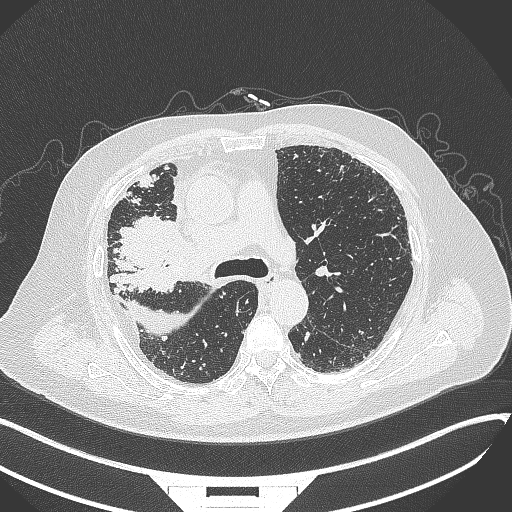
Chest CT, one axial slice; position 224 of 384 along the scan axis; reconstruction kernel B70f; 120 kVp; lung window (W 1500 / L -600 HU); 1 mm slice thickness; 512 × 512 image matrix, field of view 400 × 400 mm. Male patient, age 69 years. Case-level facts recorded for this patient, not image findings: clinical TNM (as recorded): T4 N3 M1.
Annotated regions visible in this slice (bounding box drawn by a radiologist):
- lung tumour (recorded histology: adenocarcinoma): bounding box (x1, y1, x2, y2) in pixels: (109, 217, 181, 269)